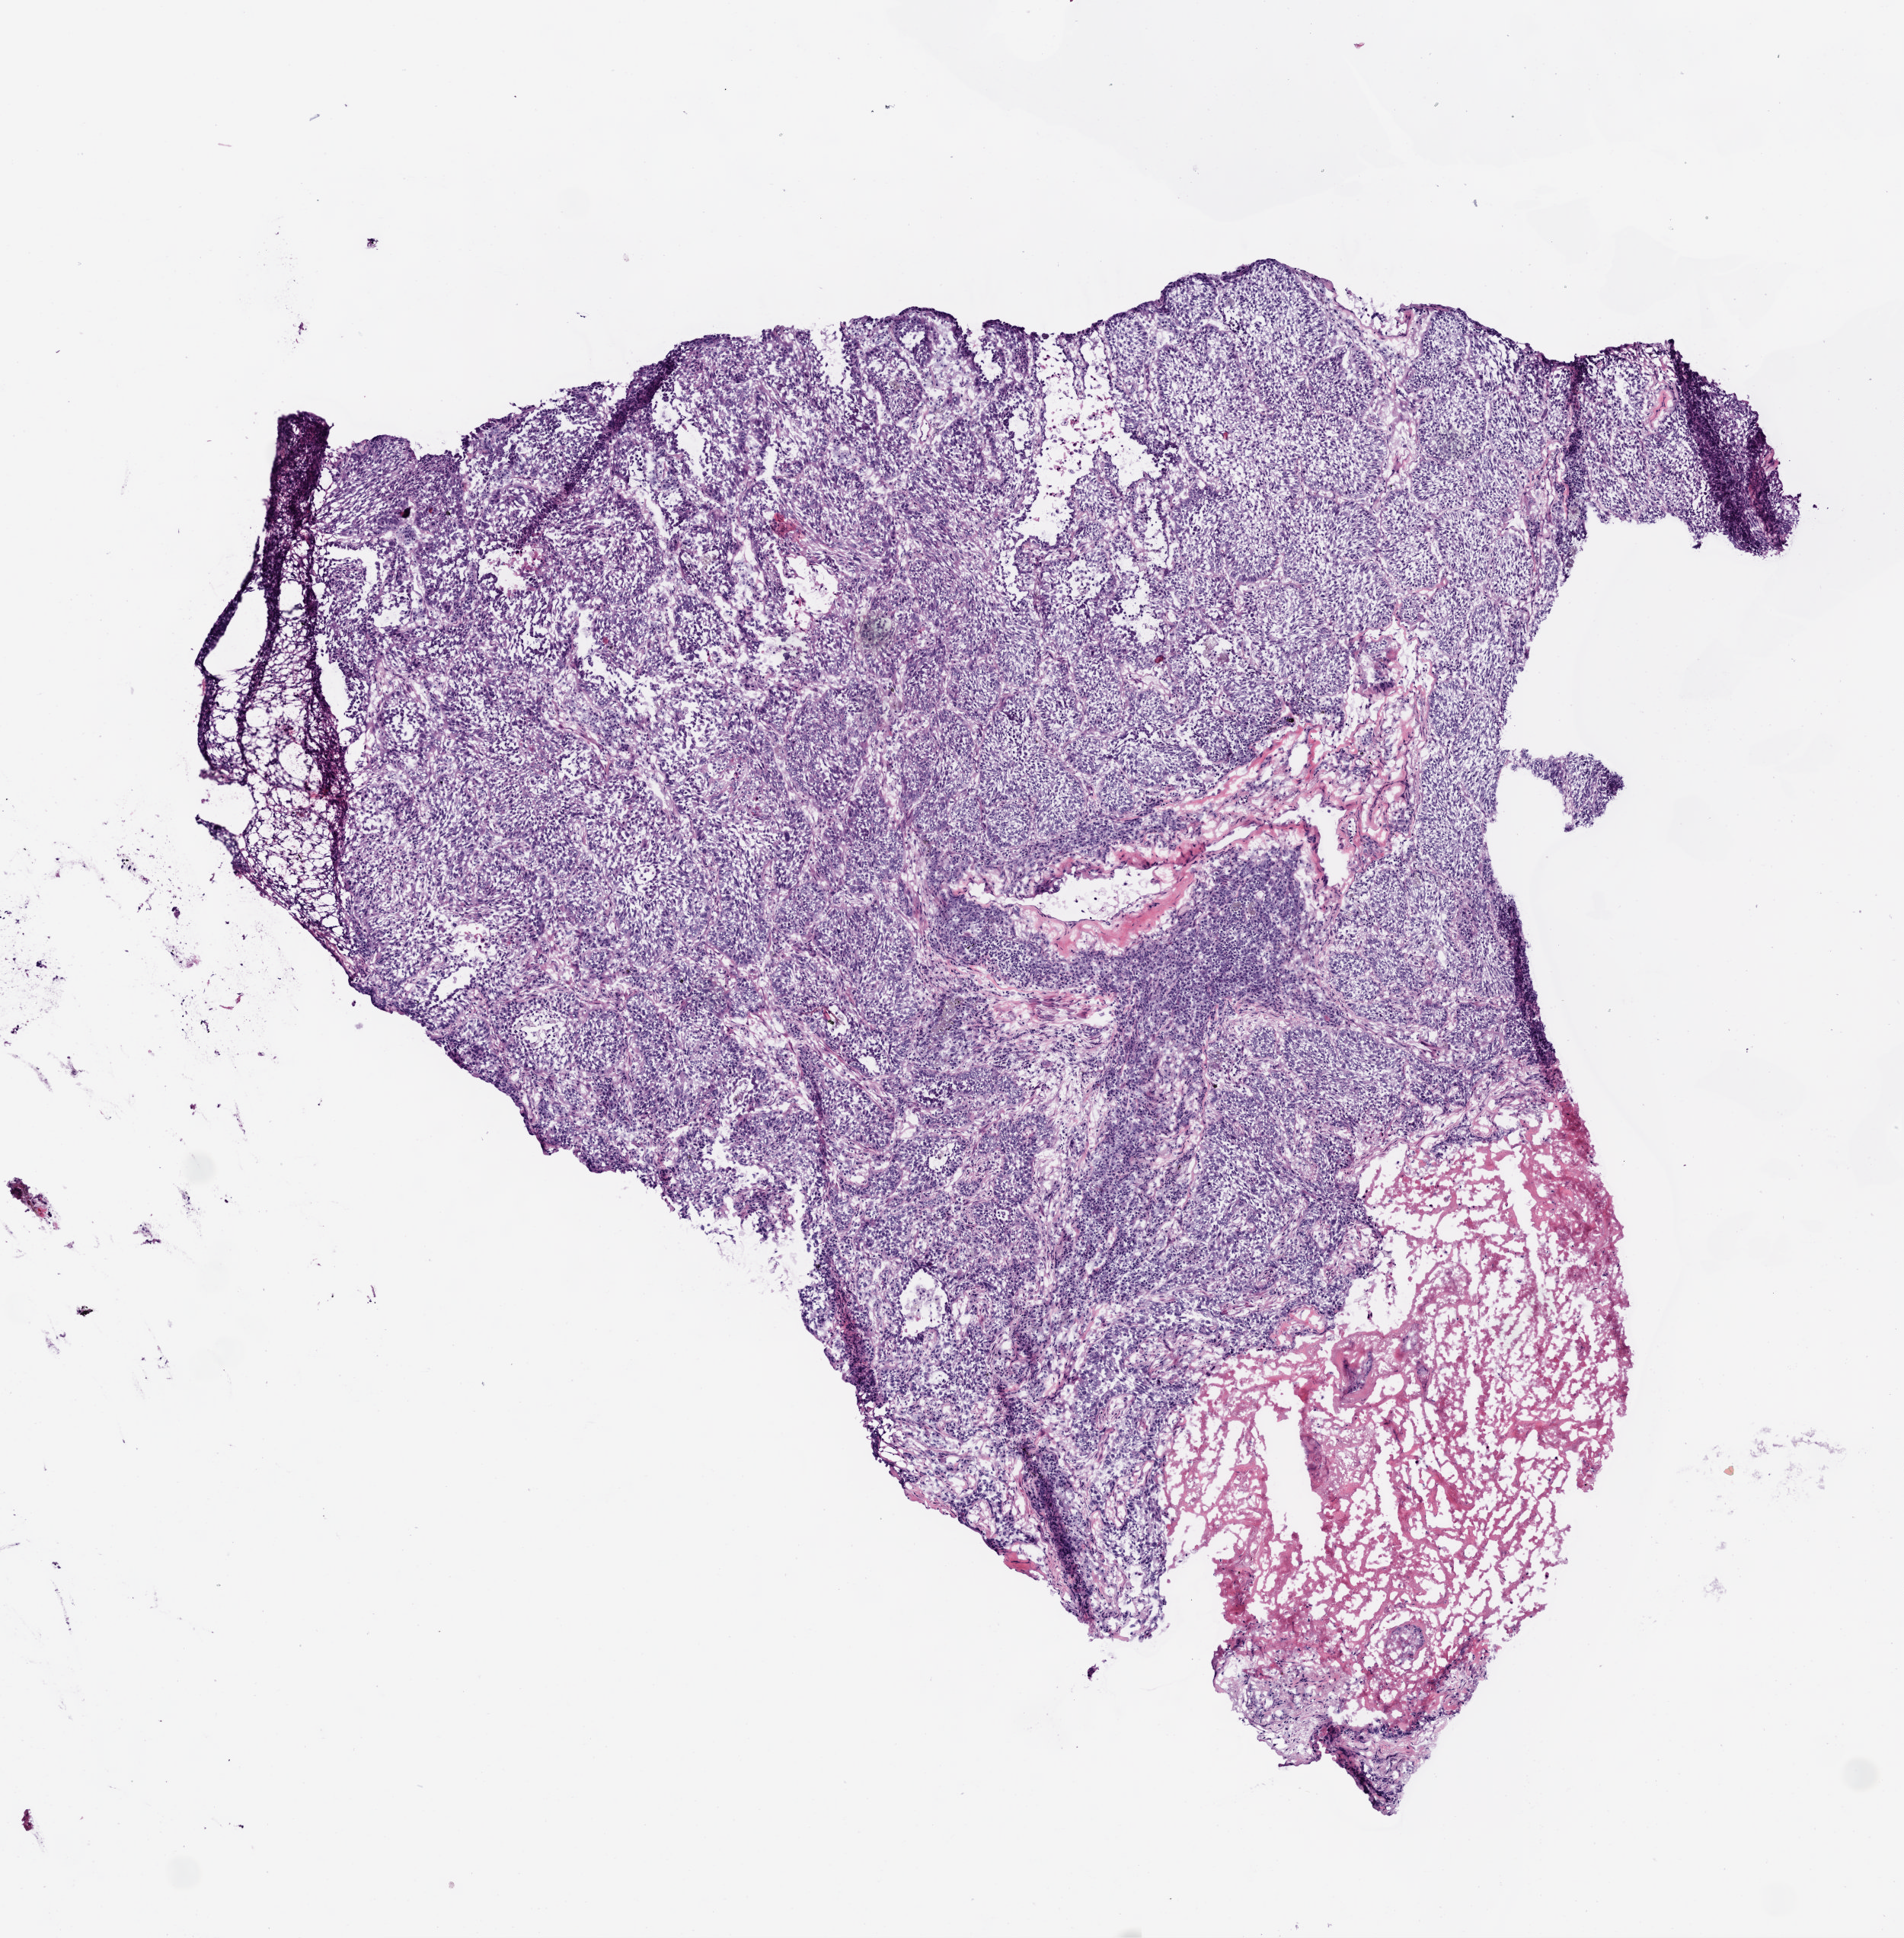
Digitized Hematoxylin and eosin (H&E) stained tissue section (whole slide) — a low-resolution overview of the entire scanned area, about 5.0 x 5.1 mm. Frozen section from the bottom of the tissue portion. Lung, primary tumour sample. Patient: female, age at initial diagnosis 77 years. Pathologist review of this section (percent, as recorded): tumour cells 80%, tumour nuclei 85%, normal cells 0%, stromal cells 10%, necrosis 10%. Infiltration values recorded for this section: lymphocyte infiltration 3%.
• laterality: right
• pathologic diagnosis: Squamous cell carcinoma, NOS (lower lobe, lung)
• AJCC pathologic stage: IB